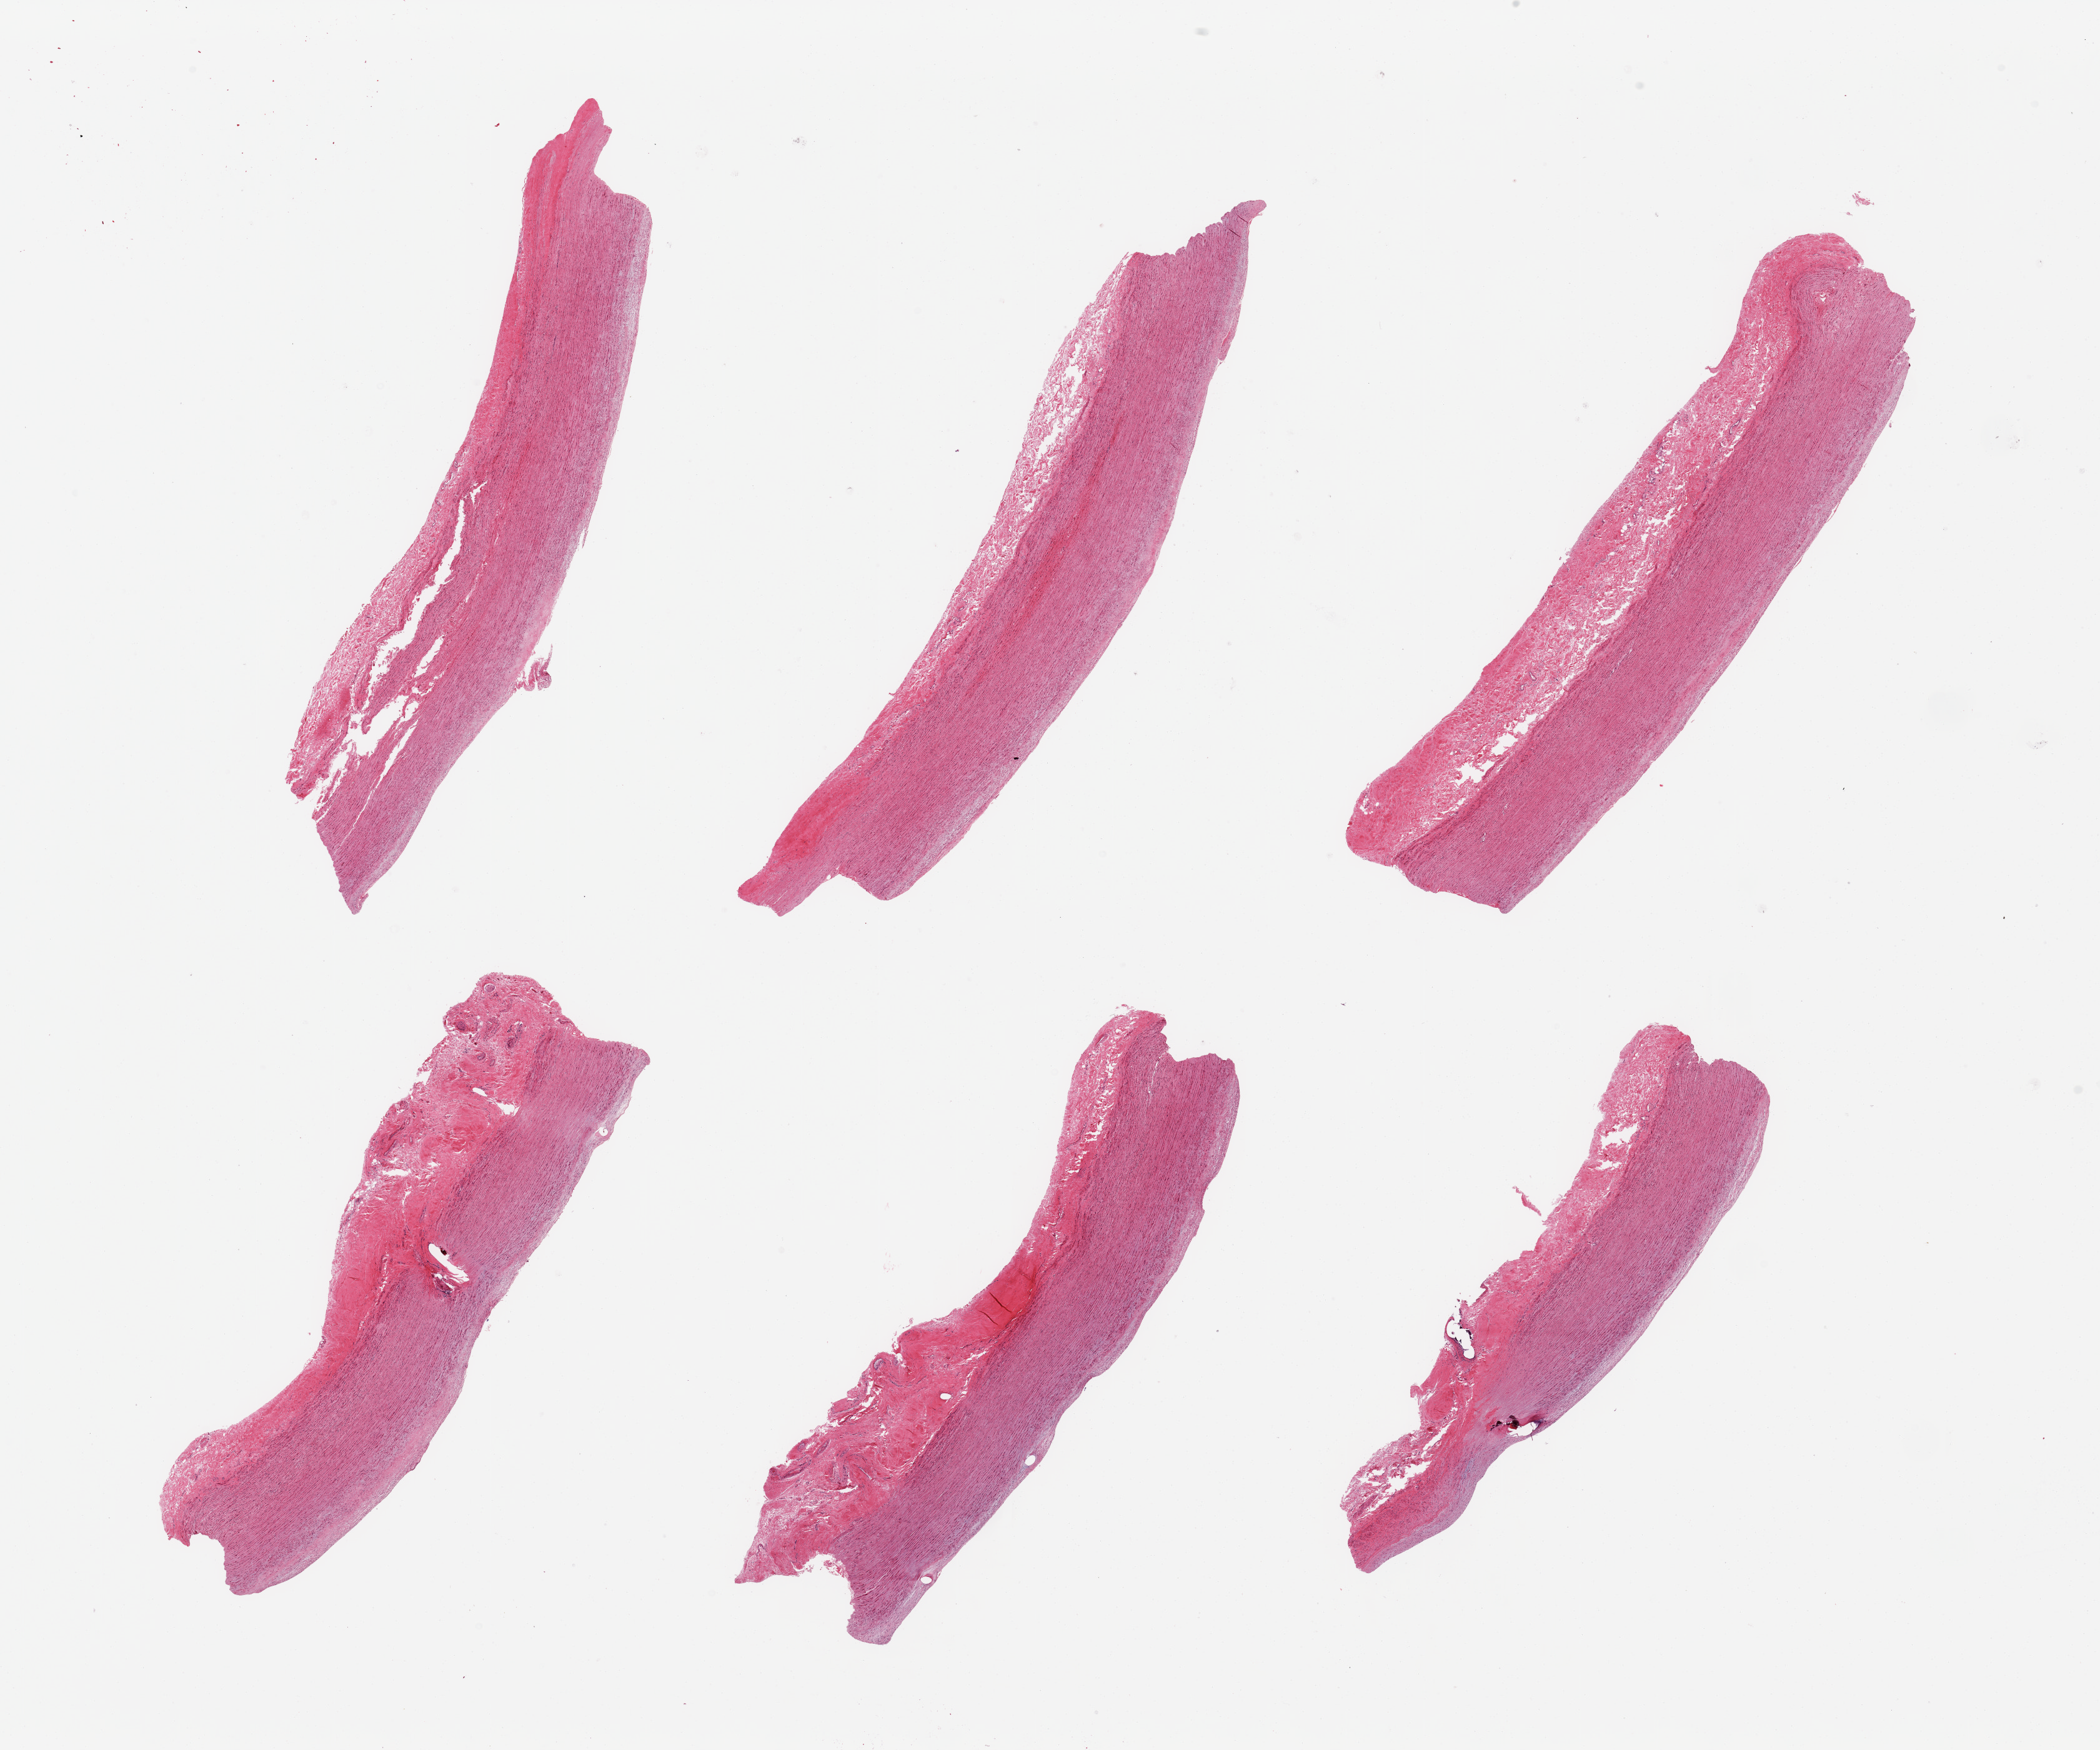
Digitized haematoxylin and eosin-stained section, brightfield, whole scanned area (about 26.6 x 22.2 mm) shown as a low-resolution overview; PAXgene-fixed paraffin-embedded (PFPE) section; section of aorta (target tissue); donor tissue sample. Male donor.
Pathologist's review note for this sample: 6 pieces; flat plaques; focal calcification associated with mural scar; 1 mm thick fibrous adventitia.